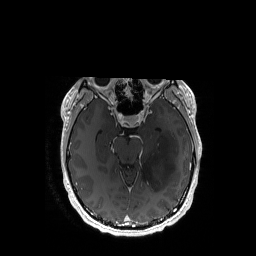
Brain MRI from a brain-tumour surgery series, one axial slice. Slice 107 of 192 in the series (ordered by position). T1-weighted post-contrast. 1 mm slice thickness. 256 × 256 image matrix, field of view 256 × 256 mm. Case-level facts recorded for this patient, not image findings: histopathology: Astrocytoma; WHO grade: 3; IDH mutation: yes.
Outlined on this slice (outlined manually by an expert reader):
- tumour: box from (x=141, y=131) to (x=178, y=191) px